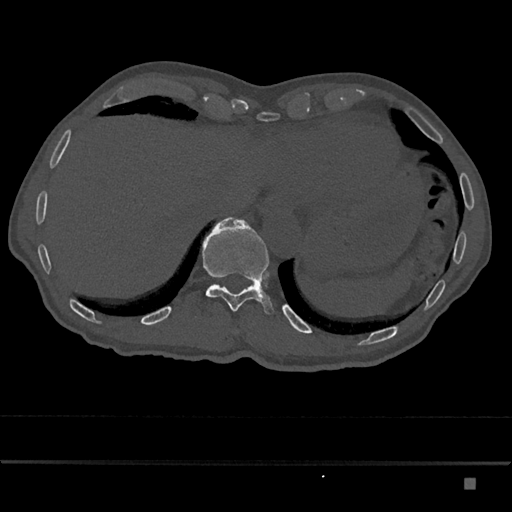
CT including the spine, one axial slice. Slice 678 of 797 in the series (ordered by position). Reconstruction kernel Br40s/3. Bone window (W 1800 / L 400 HU). 0.5 mm slice thickness. 512 × 512 image matrix, field of view 390 × 390 mm. Male patient, age 72 years. From the clinical record (not read from this slice): primary cancer: prostate.
Structures marked on this image (semi-automatically segmented with operator editing):
- T11 vertebra: bounding box (x1, y1, x2, y2) in pixels: (202, 217, 274, 314)